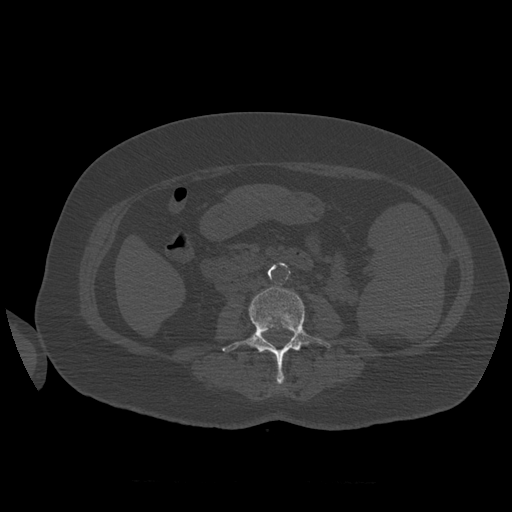
CT including the spine, one axial slice. Position 230 of 399 along the scan axis. Reconstruction kernel STANDARD. 120 kVp. Bone window (W 1800 / L 400 HU). 1.25 mm slice thickness. 512 × 512 image matrix, field of view 404 × 404 mm. Patient age 81 years. Case-level facts recorded for this patient, not image findings: primary cancer: renal; vertebrae with lytic lesions (as recorded): L1.
Structures marked on this image (semi-automatic segmentation, software-assisted and operator-edited):
- L3 vertebra: bounding box [x1, y1, x2, y2] px = [223, 287, 331, 384]